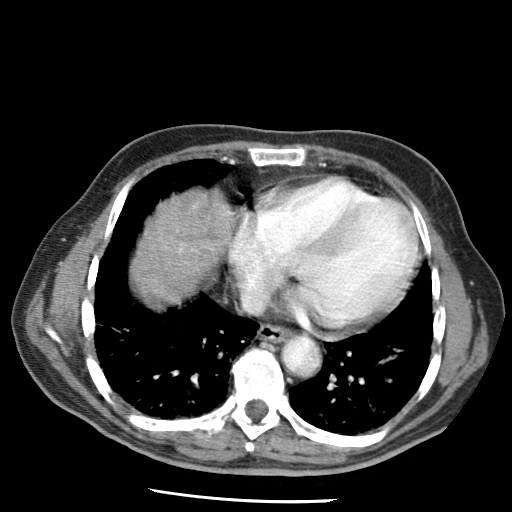
Contrast-enhanced abdominal CT (liver protocol), one axial slice. 120 kVp. Soft-tissue window (W 400 / L 40 HU). 2.5 mm slice thickness. 512 × 512 image matrix, field of view 320 × 320 mm. From the clinical record (not read from this slice): diagnosis: hepatocellular carcinoma (patient treated with transarterial chemoembolisation; whether this scan precedes or follows treatment is not stated here); TNM stage (as recorded): Stage-IIIA; Child-Pugh class: A; tumour differentiation: moderately differentiated; tumour nodularity: multinodular.
Structures marked on this image (semi-automatic segmentation, software-assisted and operator-edited):
- liver parenchyma outside the tumour (the mass and vessels are separate outlines, so this box may not span the whole liver): bounding box <130,192,234,302> (left, top, right, bottom; pixels)
- liver vessels: <179,211,230,252>